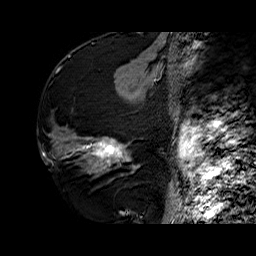
Breast MRI (dynamic contrast-enhanced), one sagittal slice; dynamic contrast-enhanced series, time point 2 of 6 at this slice position (early post-contrast); 1.5 T; TE 6.4 ms, TR 32.7 ms; 256 × 256 image matrix. Female patient. From the clinical record (not read from this slice): setting: breast cancer imaged before/during neoadjuvant chemotherapy; receptor status: HR-positive, HER2-negative.
Structures marked on this image (semi-automatically segmented with operator editing):
- analysis volume of interest (the breast-tissue region the enhancement analysis was run in; not a lesion): bounding box [x1, y1, x2, y2] px = [73, 133, 141, 177]
- tumour enhancement mask (voxels above the 100 % enhancement threshold inside the analysis volume of interest): [86, 138, 130, 166]